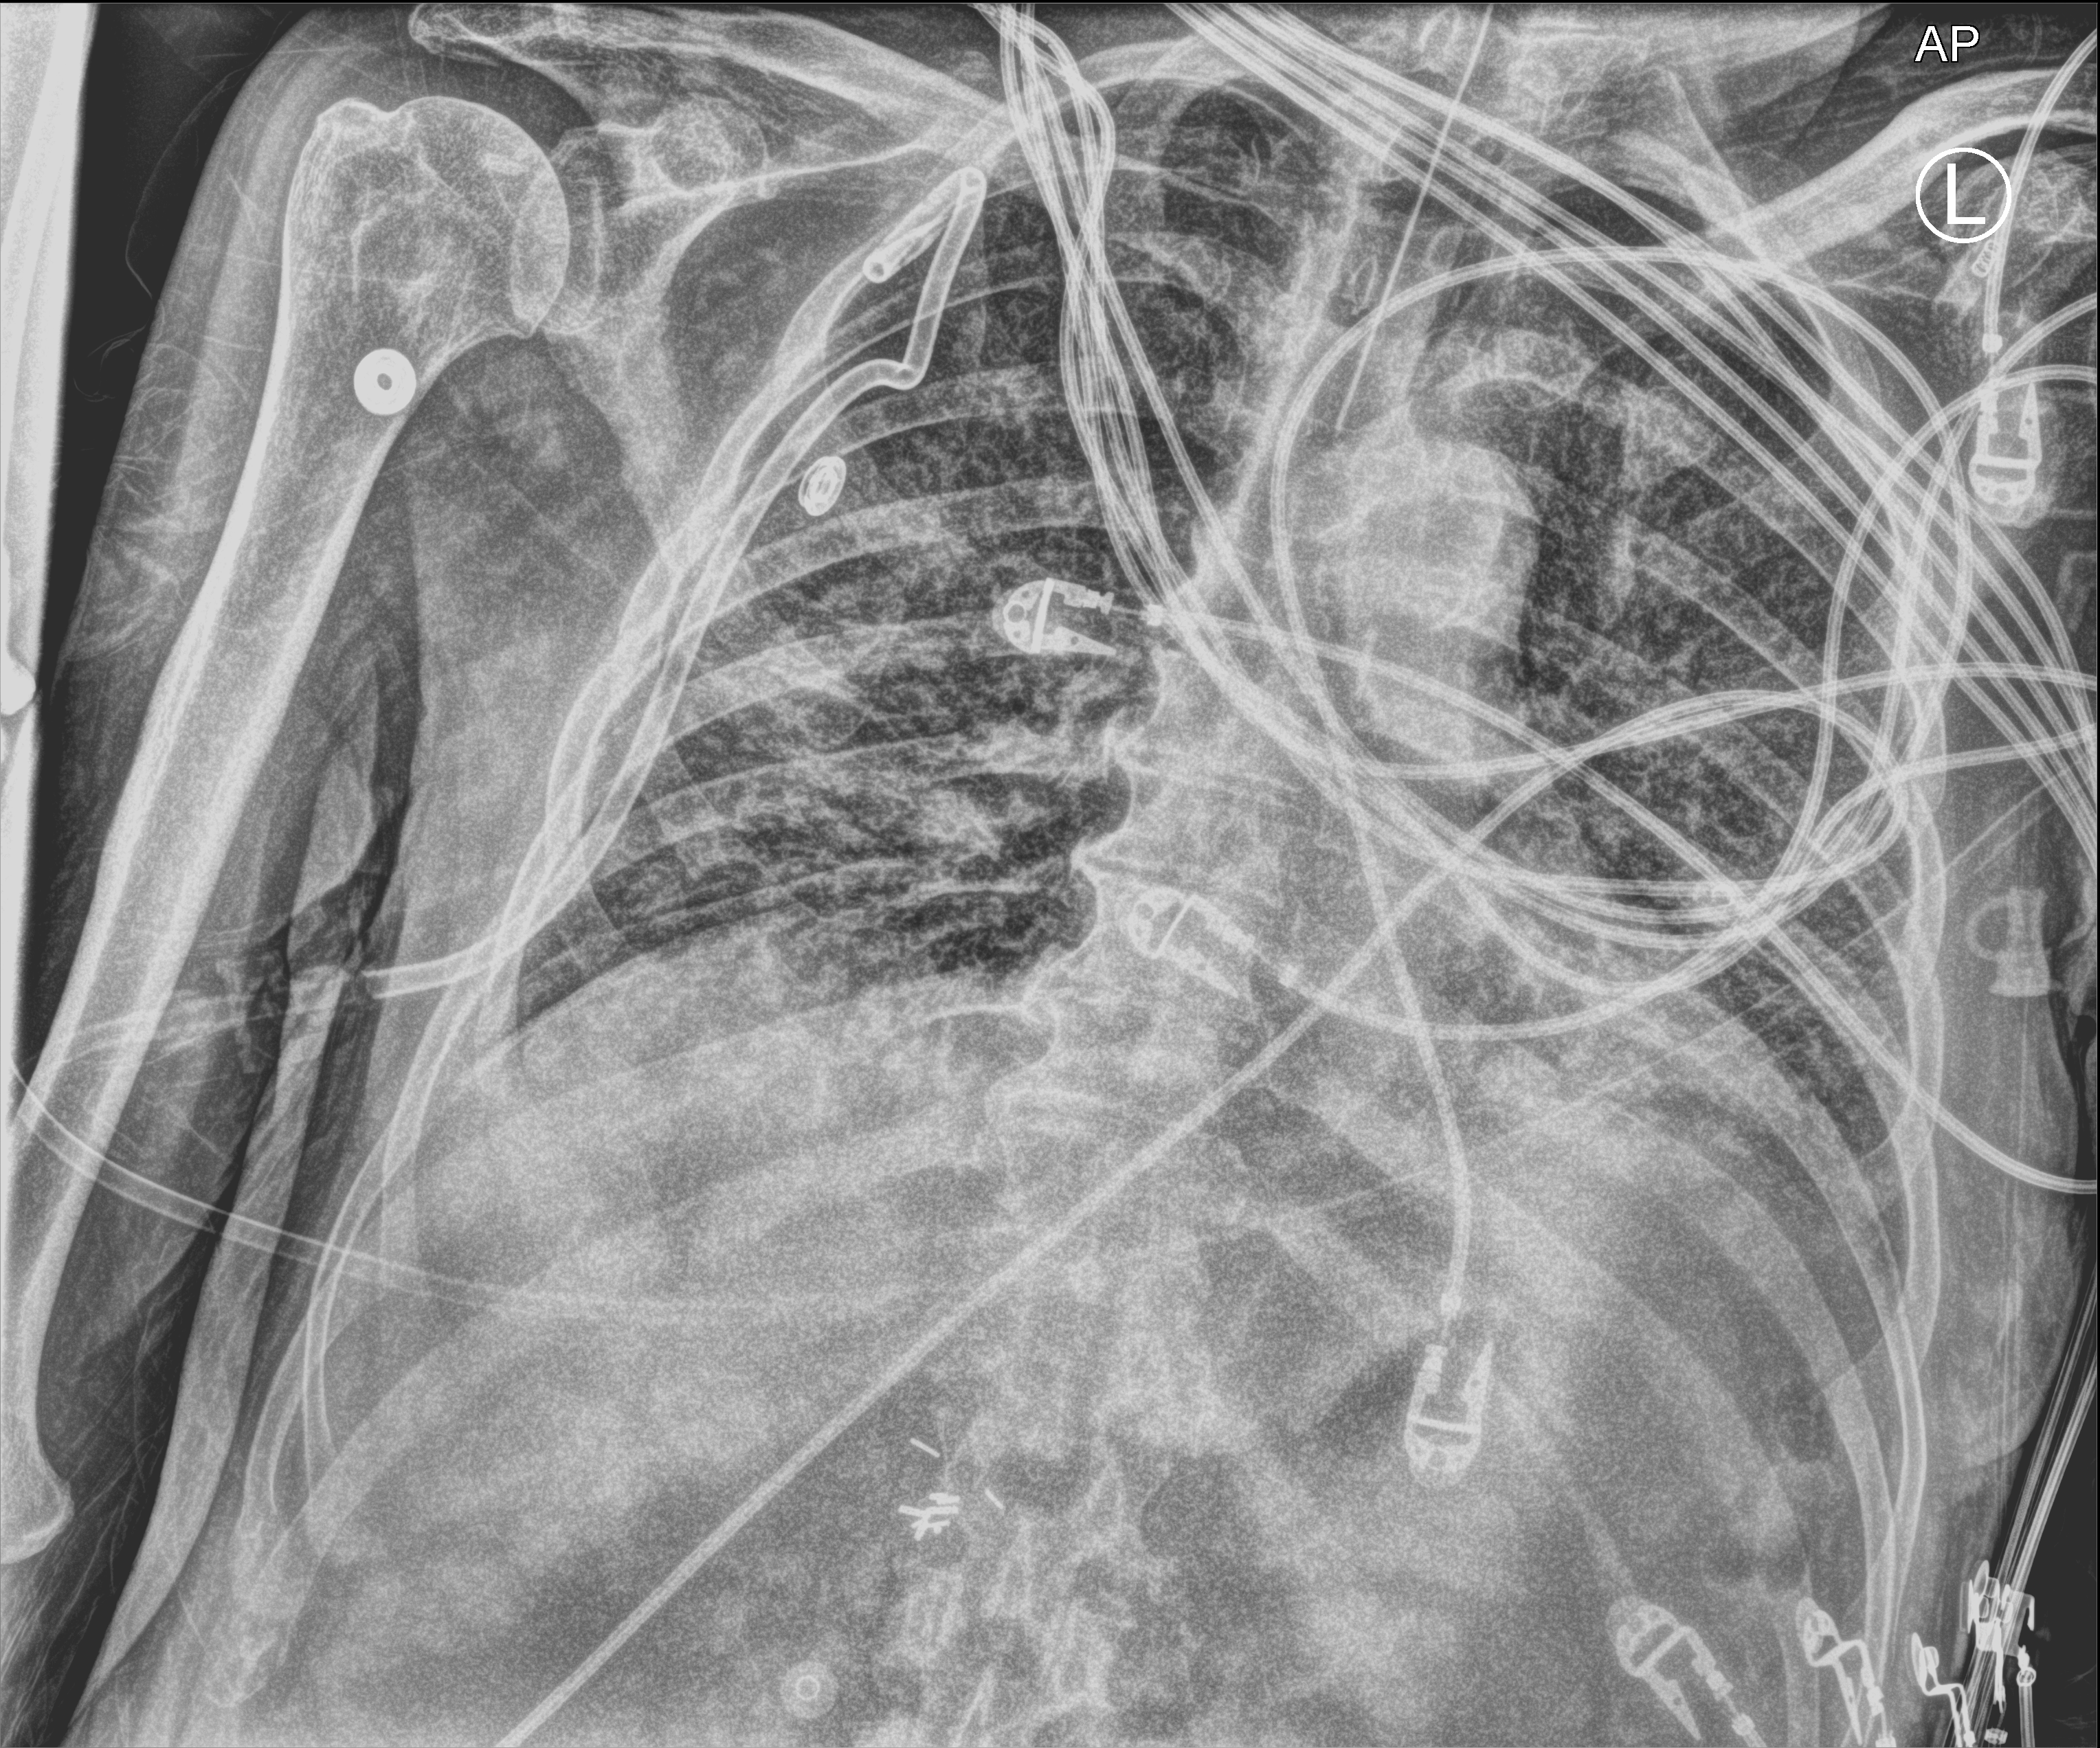
Bedside chest radiograph (computed radiography), anteroposterior (AP) projection. Male patient hospitalised with COVID-19, age 75–90 years.
Hospital-stay facts (about this admission, not read from this image; timing relative to this image not recorded): admitted to intensive care during this hospital stay: yes; mechanically ventilated during this hospital stay: yes; length of hospital stay: 23 days.